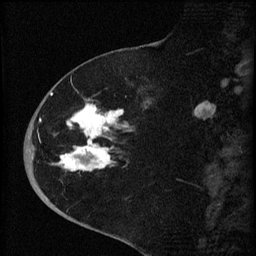
Breast MRI (dynamic contrast-enhanced), one sagittal slice; position 26 of 60 along the scan axis; dynamic contrast-enhanced series, image 2 of 4 at this slice position (ordered by acquisition); 1.5 T; TE 4.2 ms, TR 8.2 ms; 2 mm slice thickness; 256 × 256 image matrix, field of view 180 × 180 mm. Female patient, age 71 years.
Structures marked on this image (semi-automatically segmented with operator editing):
- analysis volume of interest (the breast-tissue region the enhancement analysis was run in; not a lesion): bounding box <35,75,153,190> (left, top, right, bottom; pixels)
- tumour enhancement mask (voxels above the 70 % enhancement threshold inside the analysis volume of interest): <50,92,128,172>